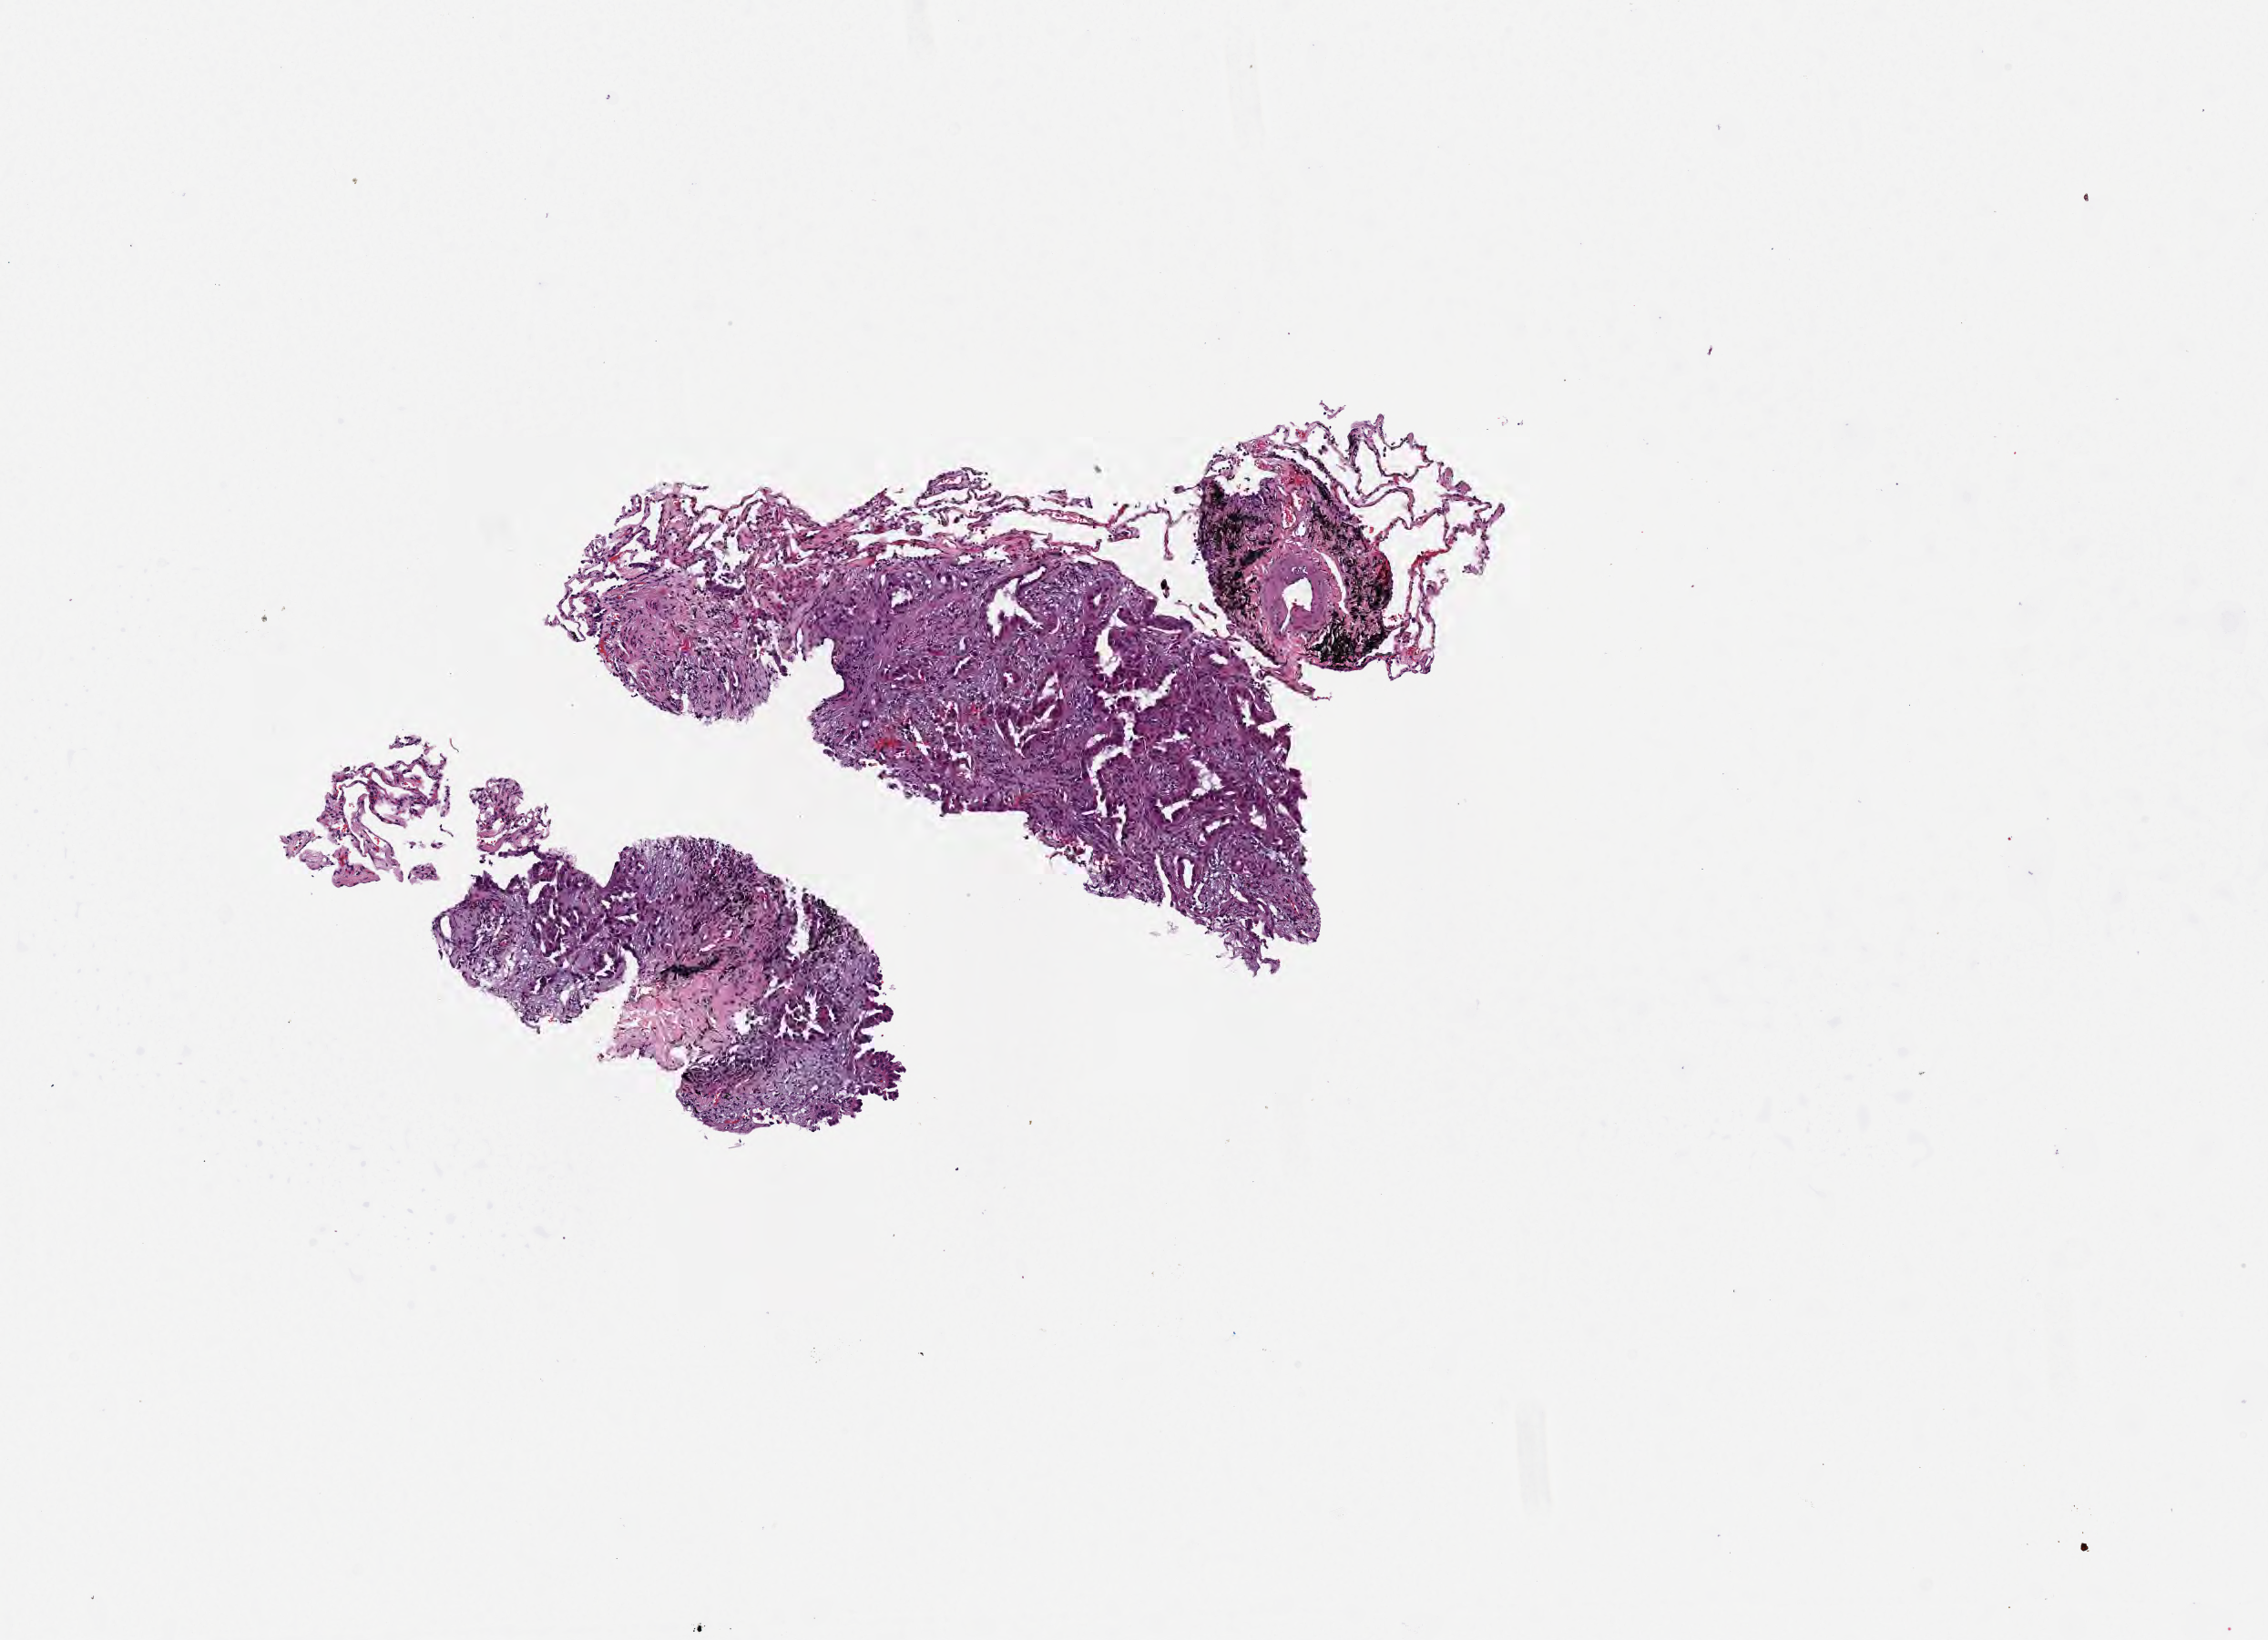
Digitized hematoxylin and eosin (H&E)-stained section, a low-resolution overview of the entire scanned area, about 5.0 x 3.6 mm; tumor tissue; site: lung (left). Patient: female, 63 years old.
Histologic diagnosis: Adenocarcinoma, NOS.